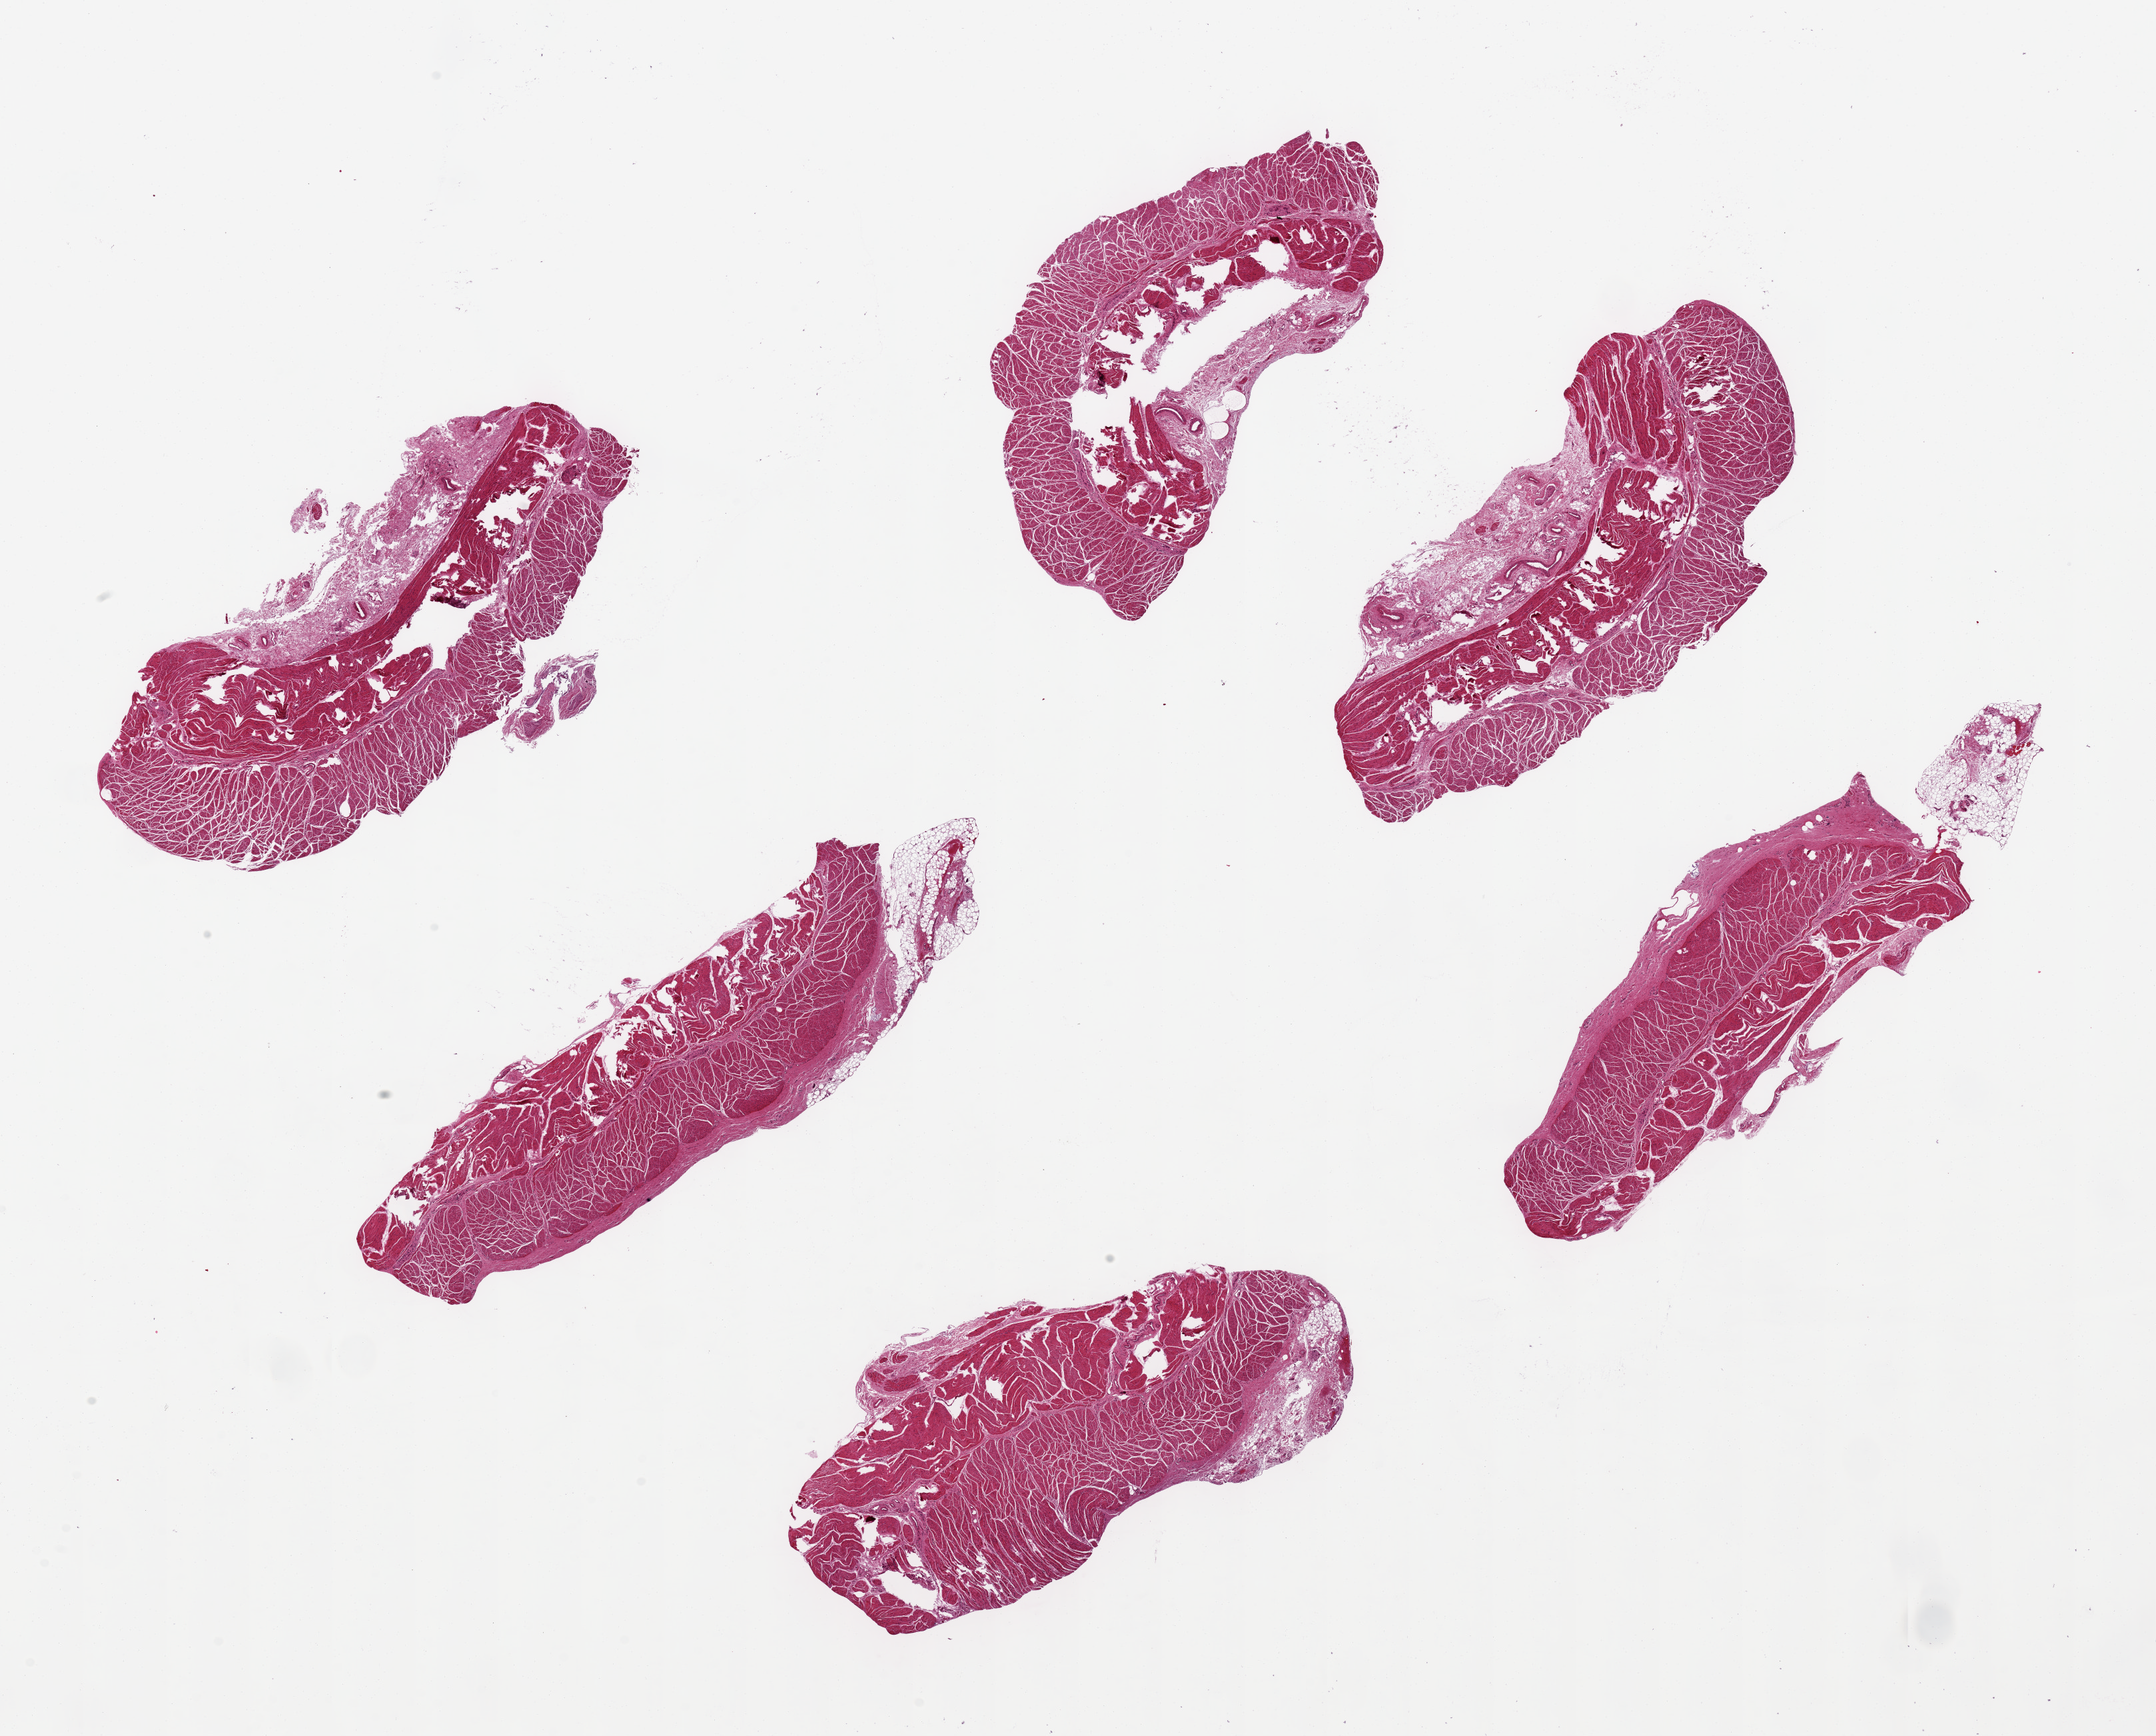
H&E whole-slide image, a low-resolution overview of the entire scanned area, about 25.6 x 20.6 mm; PAXgene-fixed, paraffin-embedded tissue; section of esophageal muscle (target tissue); tissue donor sample. Donor: female.
Pathologist's review note for this sample: 6 pieces, ~8x3mm; 5 of the 6 have major muscle fragmentation/tears.